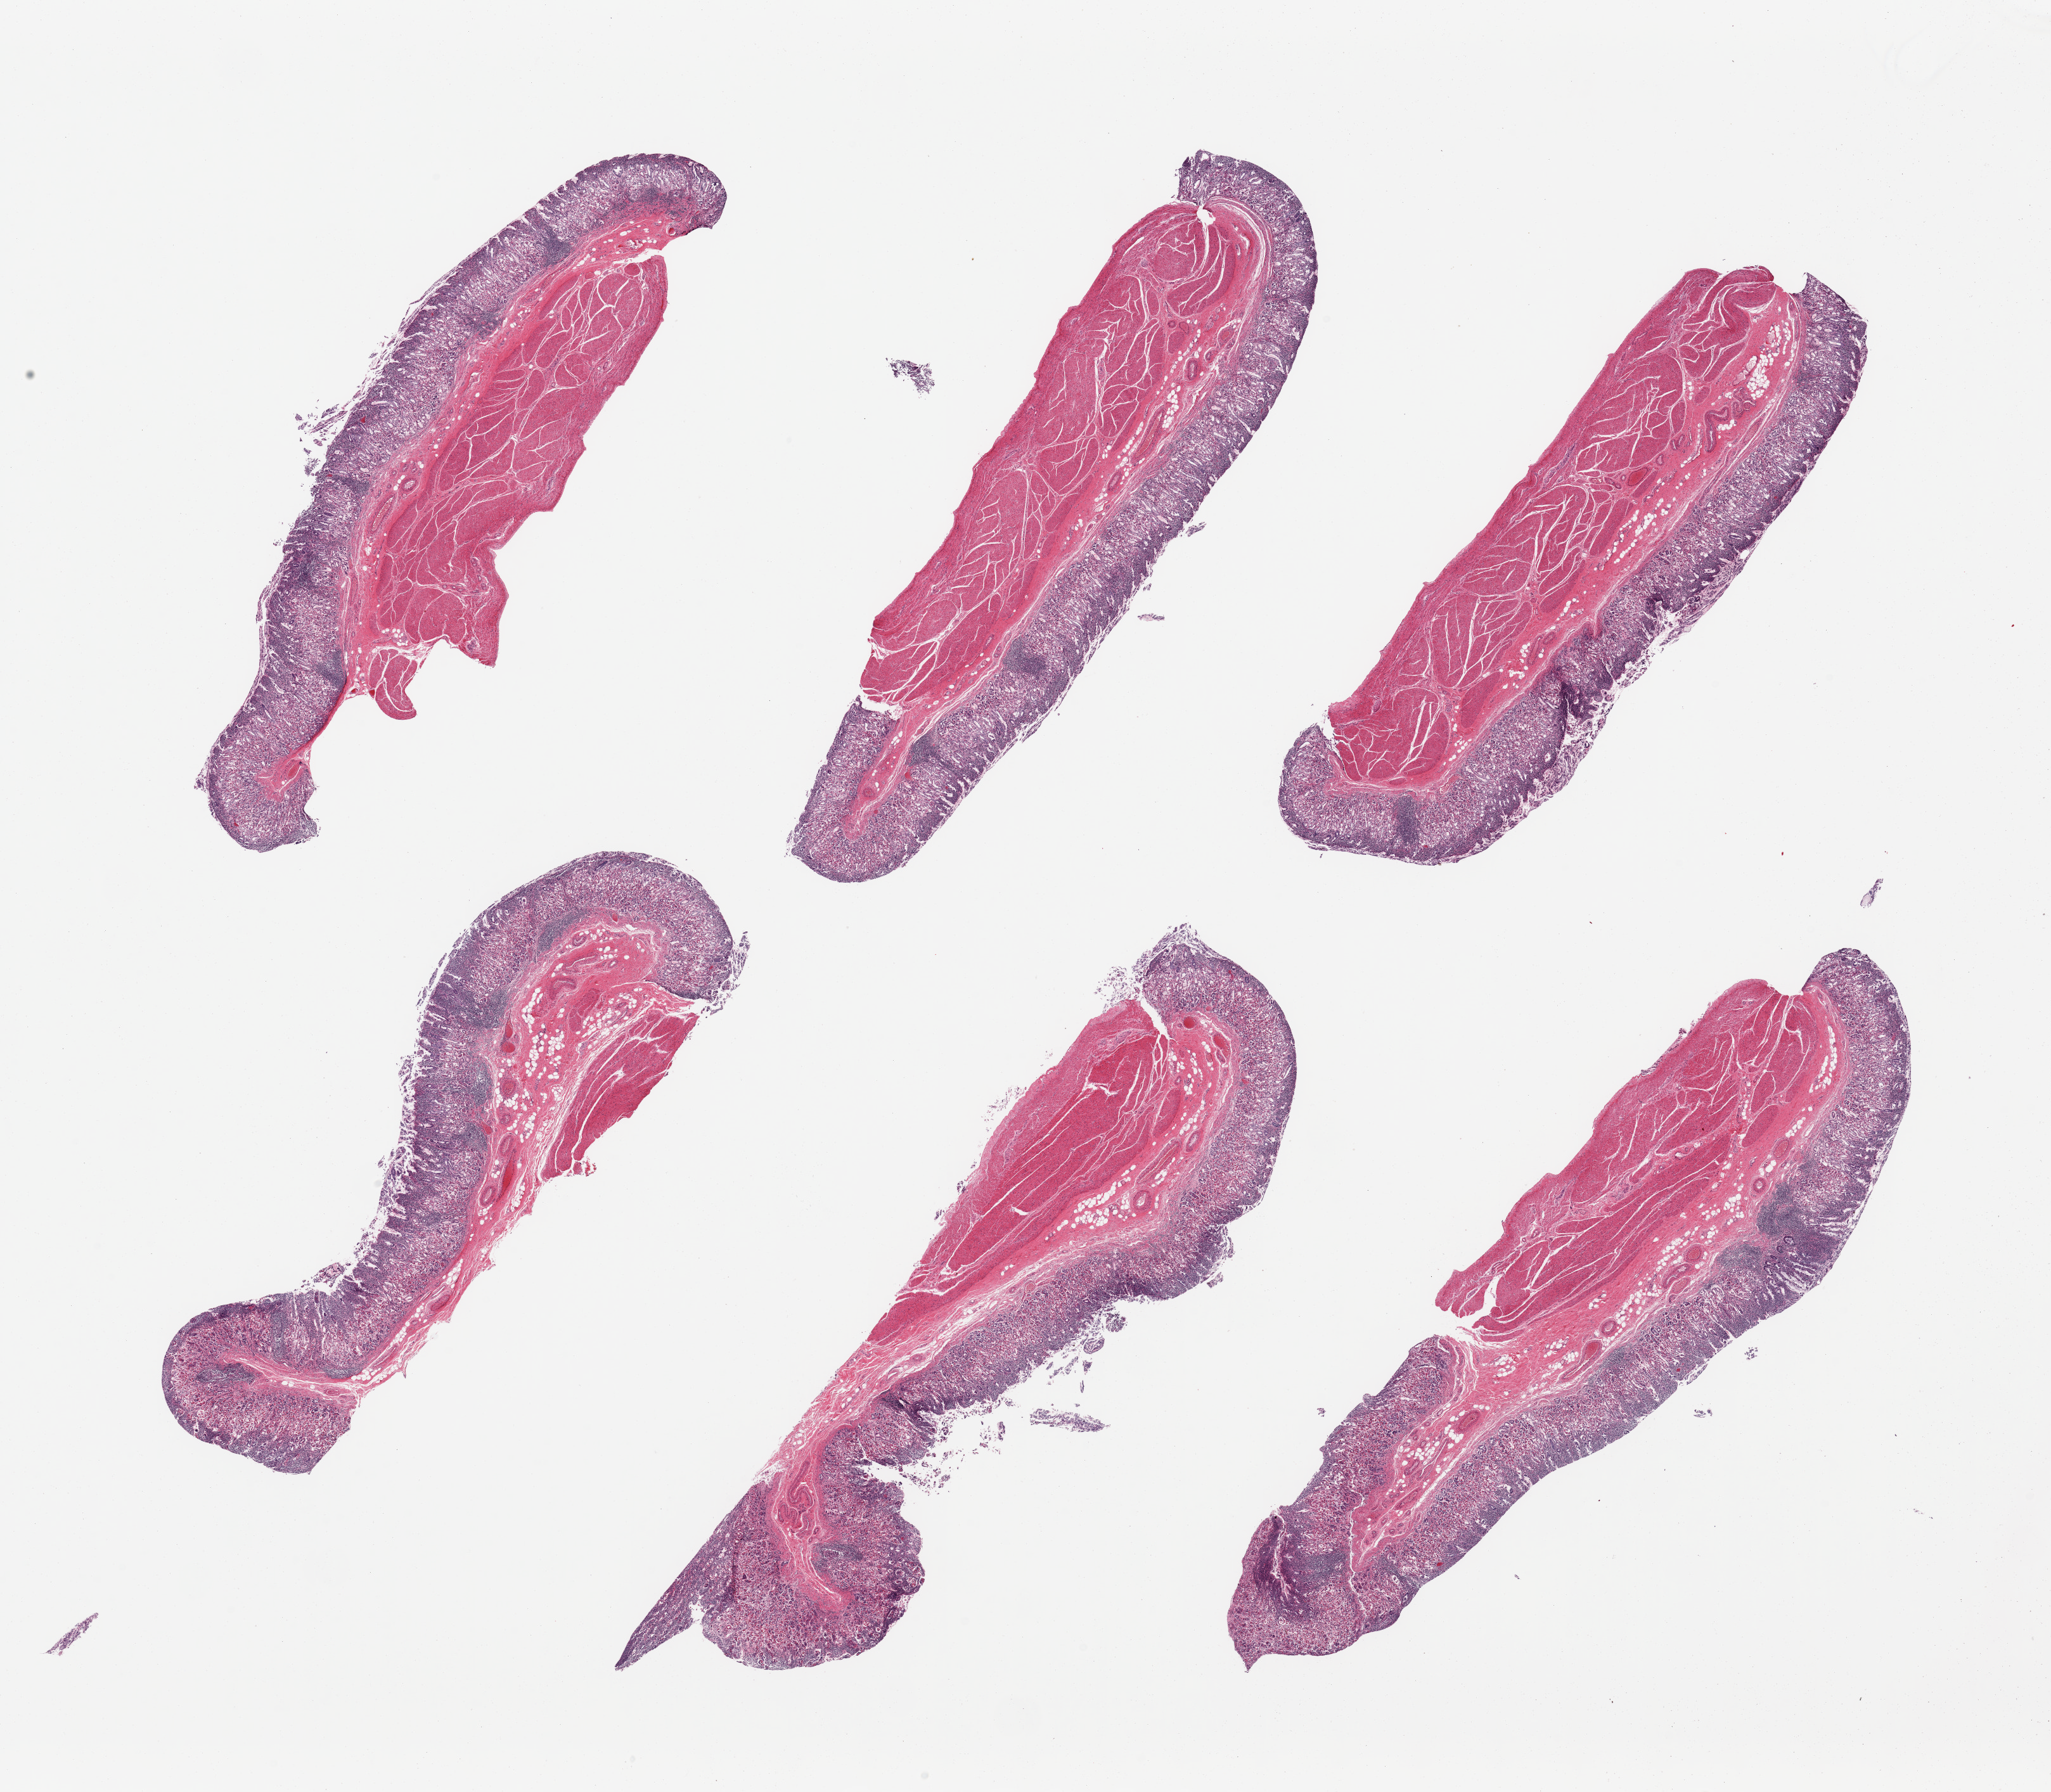
Whole-slide image, hematoxylin and eosin (H&E) stain — a low-resolution overview of the entire scanned area, about 25.6 x 22.4 mm (from a 20x scan), PAXgene-fixed, paraffin-embedded tissue, sampled site (target tissue): stomach, donor tissue sample.
Pathologist's review note for this sample: 6 pieces; moderate chronic gastritis with moderate mucosal lymphoid infiltrates.